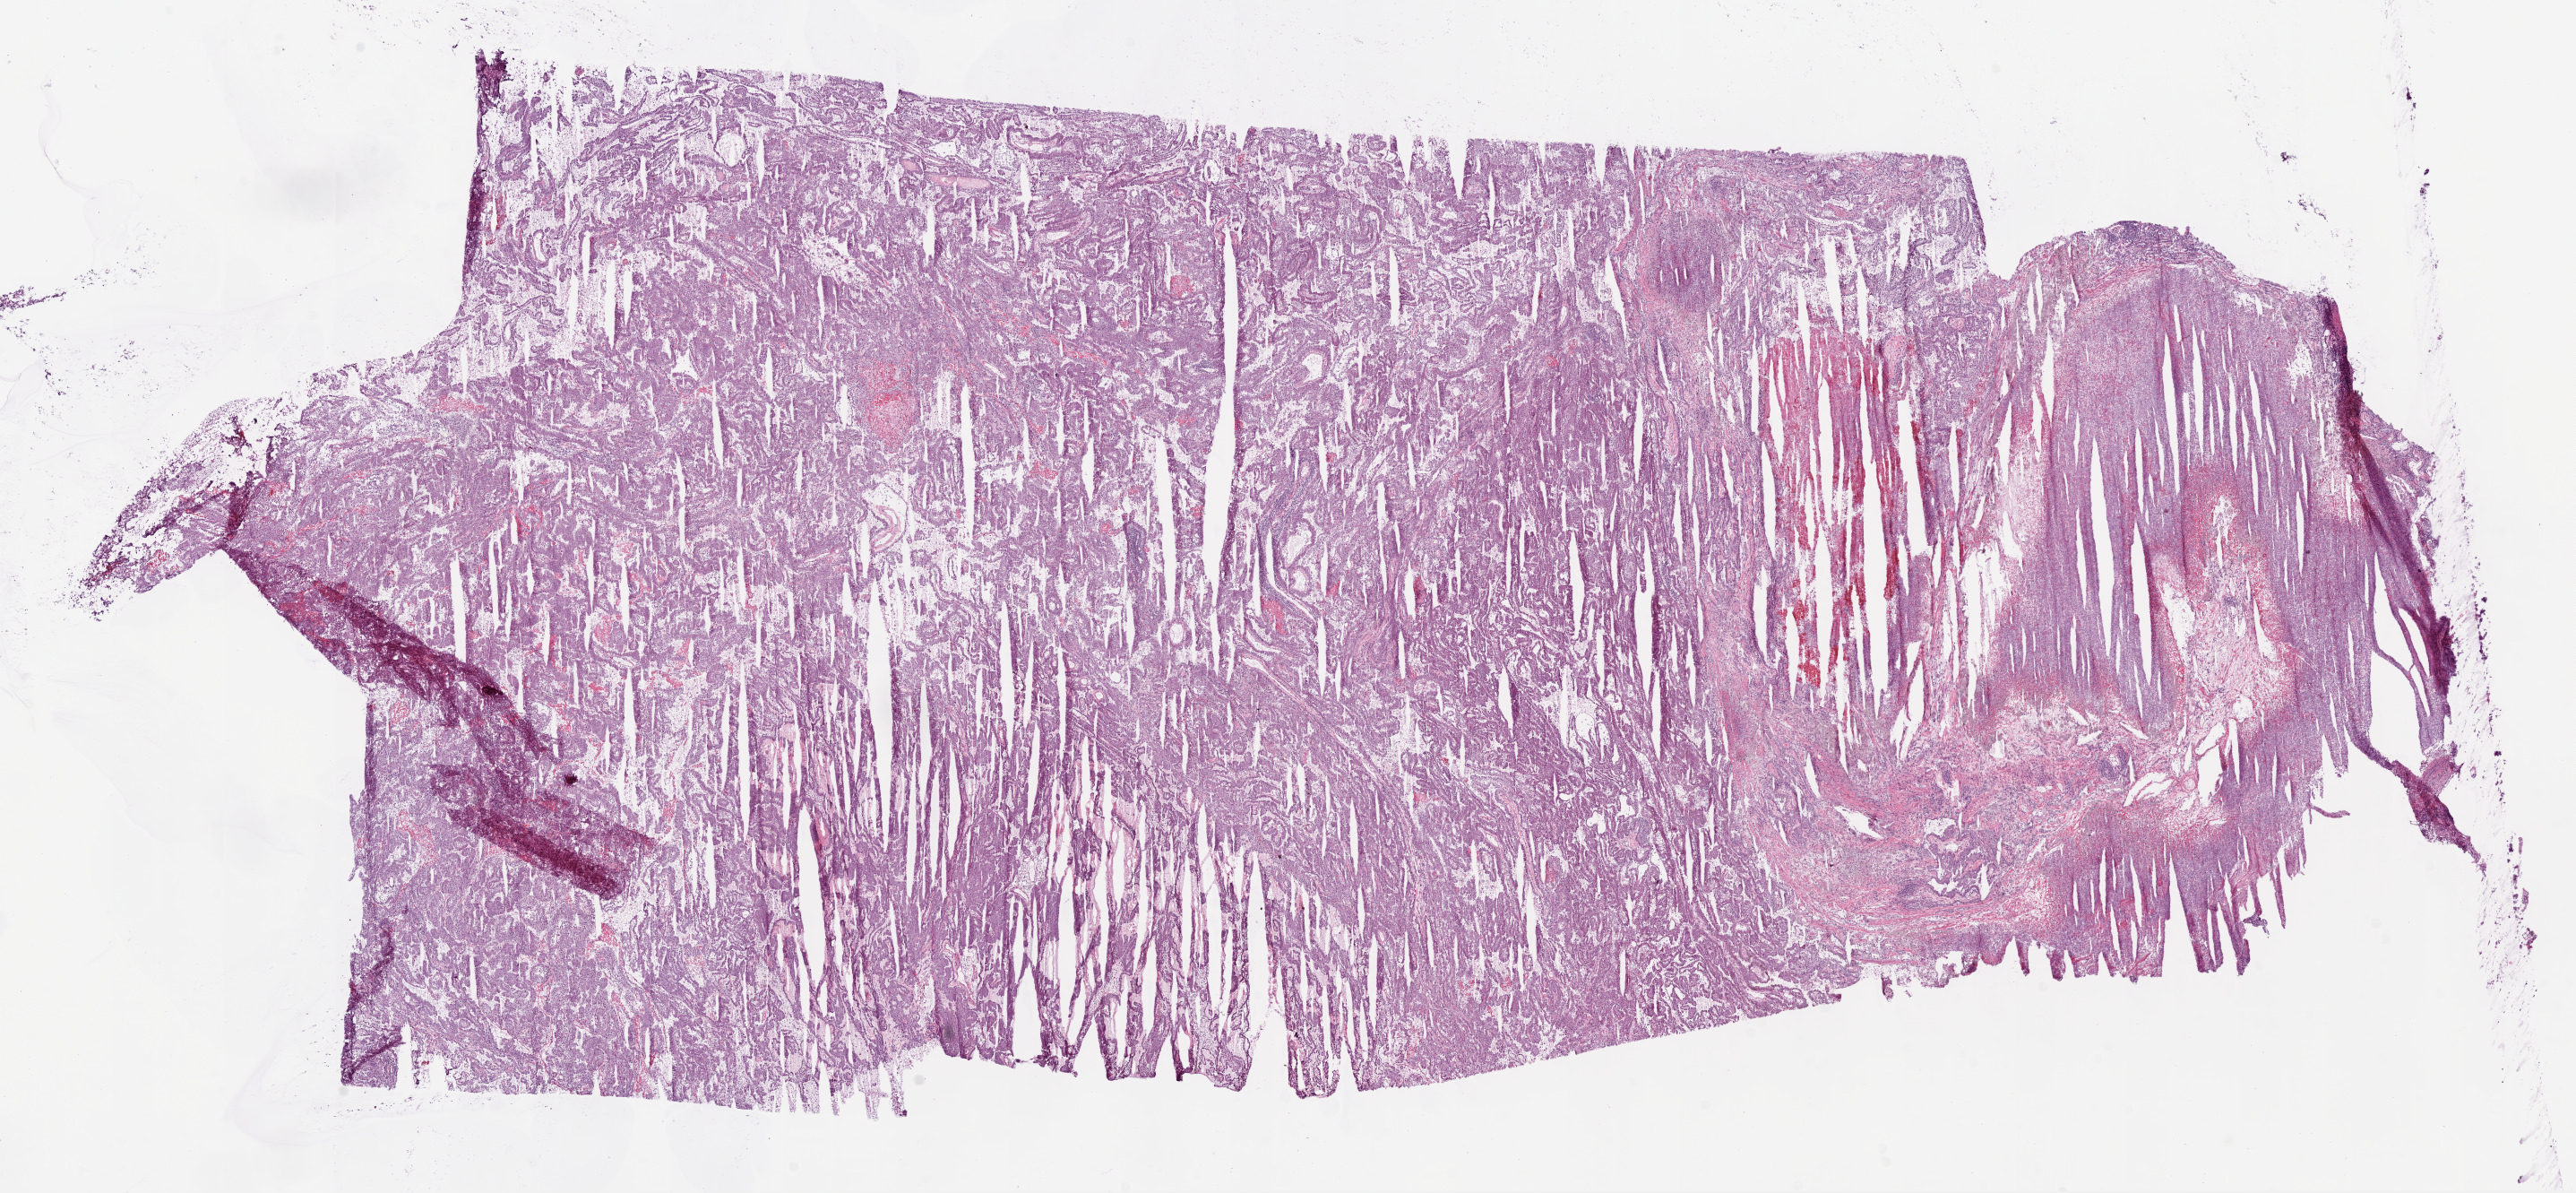
H&E whole-slide image, shown as a low-resolution overview of the whole scanned area (about 23.1 x 10.7 mm, slide scanned at 20x). Frozen section from the bottom of the tissue portion. Primary tumour sample from the kidney. Patient: female, age at initial diagnosis 72 years. Histologic grade: G2 (moderately differentiated). Pathologist review of this section (percent, as recorded): tumour cells 83%, tumour nuclei 85%, normal cells 0%, stromal cells 2%, necrosis 15%. Inflammatory infiltration, as recorded: lymphocyte infiltration 13%, monocyte infiltration 0%, neutrophil infiltration 0%.
* TNM: T1b NX M0
* AJCC pathologic stage: I
* pathologic diagnosis: Clear cell adenocarcinoma, NOS